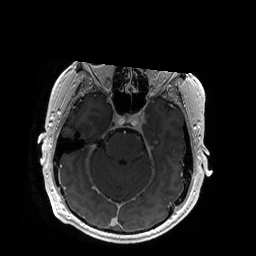
Brain MRI from a brain-tumour surgery series, one axial slice. Position 128 of 192 along the scan axis. T1-weighted post-contrast. 256 × 256 image matrix, field of view 256 × 256 mm. From the clinical record (not read from this slice): histopathology: Glioblastoma; WHO grade: 4; IDH mutation: no.
Annotated regions visible in this slice (outlined manually by an expert reader):
- tumour: bounding box <155,142,157,144> (left, top, right, bottom; pixels)